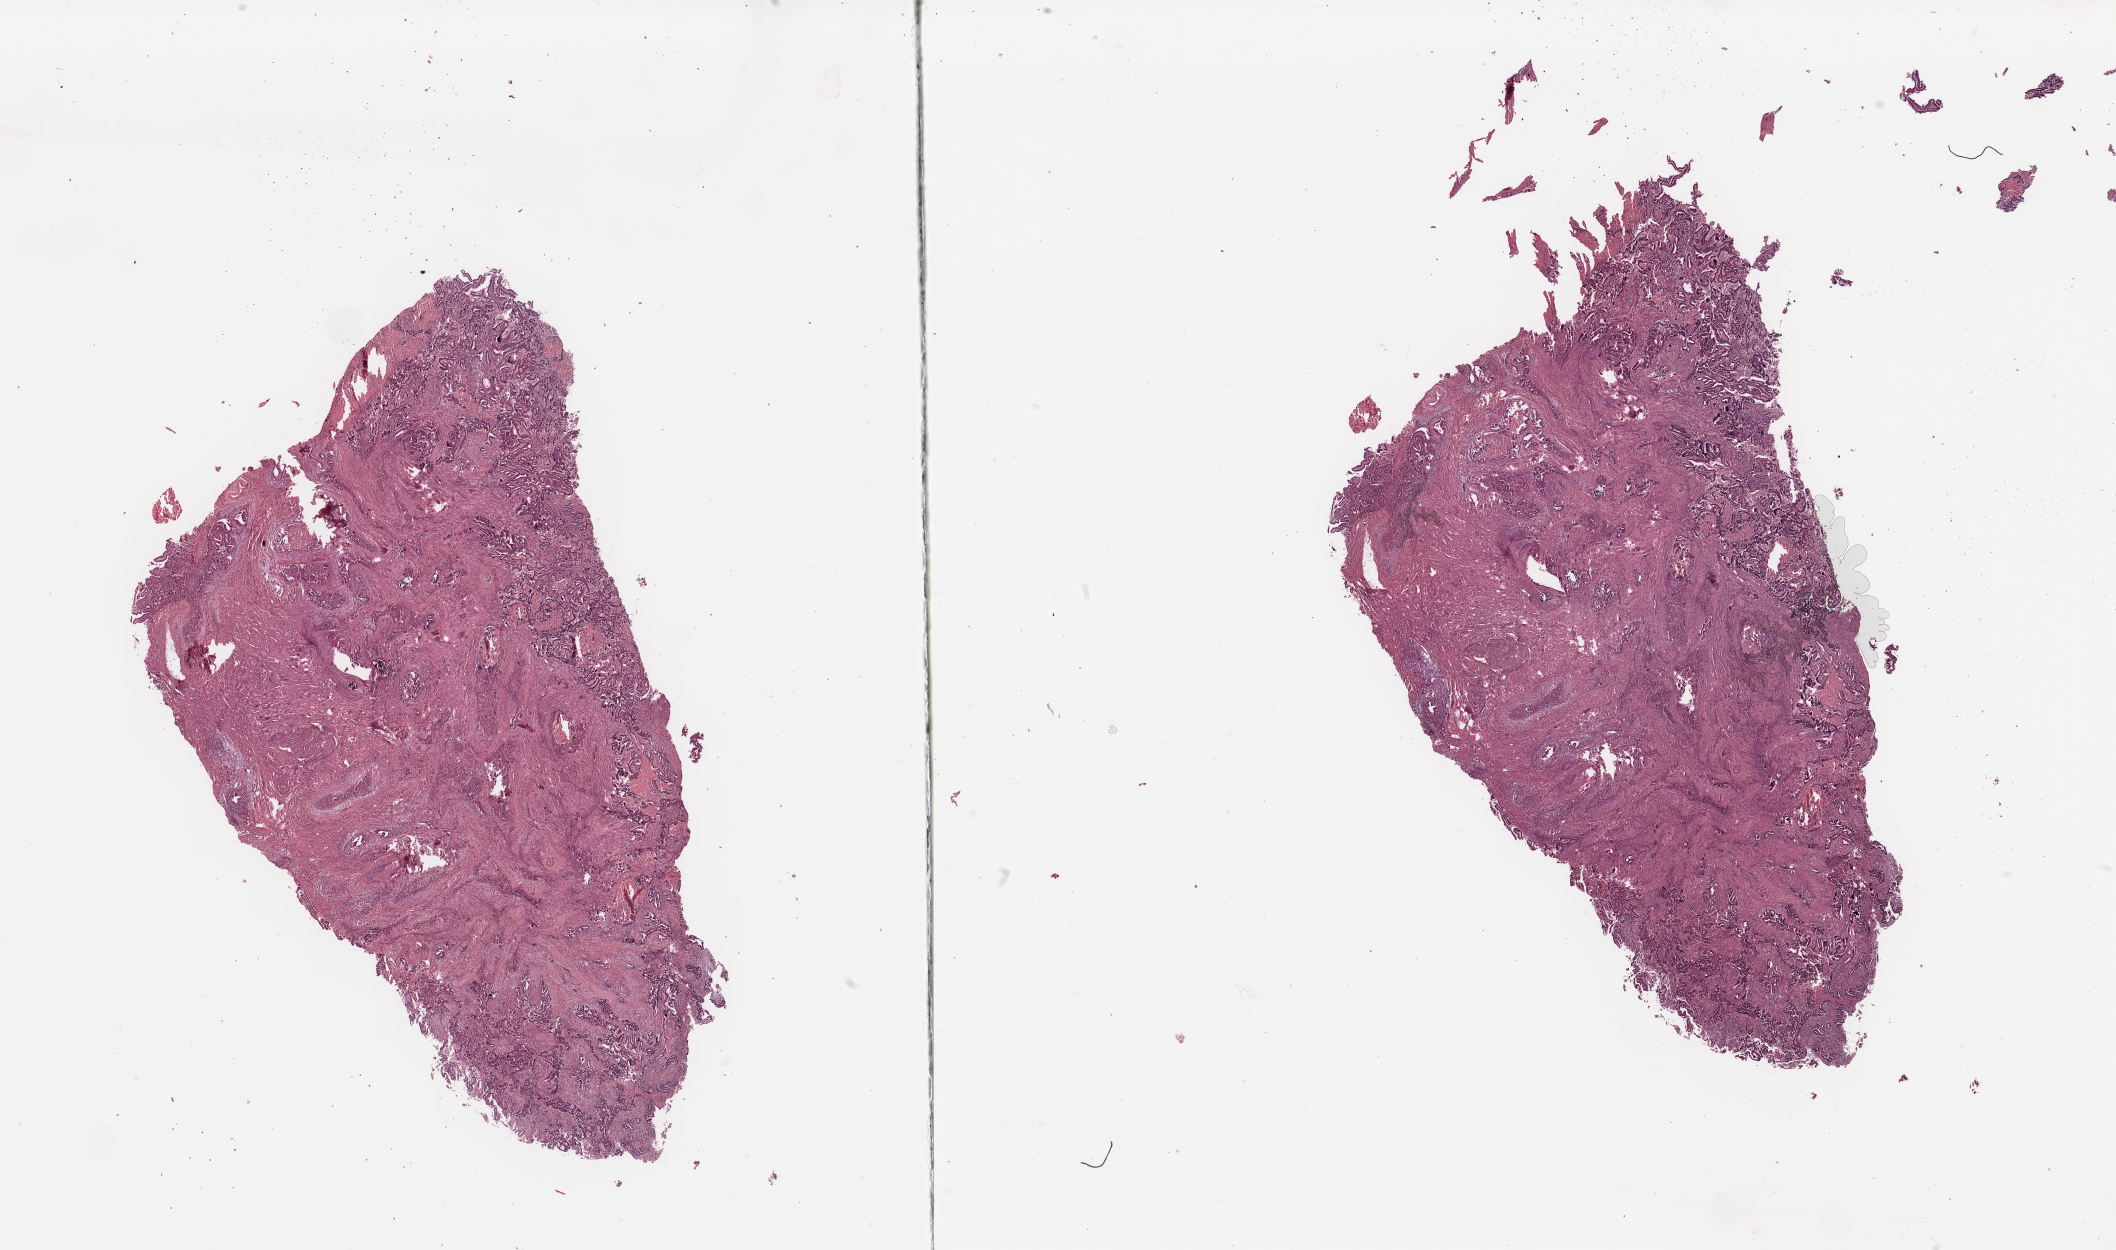
H&E-stained whole-slide image — low-resolution overview of the scanned area, about 33.5 x 19.8 mm (acquisition: 20x scan), tumour tissue sample, uterus. 54-year-old female patient. Histologic grade: G2 (moderately differentiated).
Diagnosis: Endometrioid adenocarcinoma, NOS. AJCC pathologic stage: I.